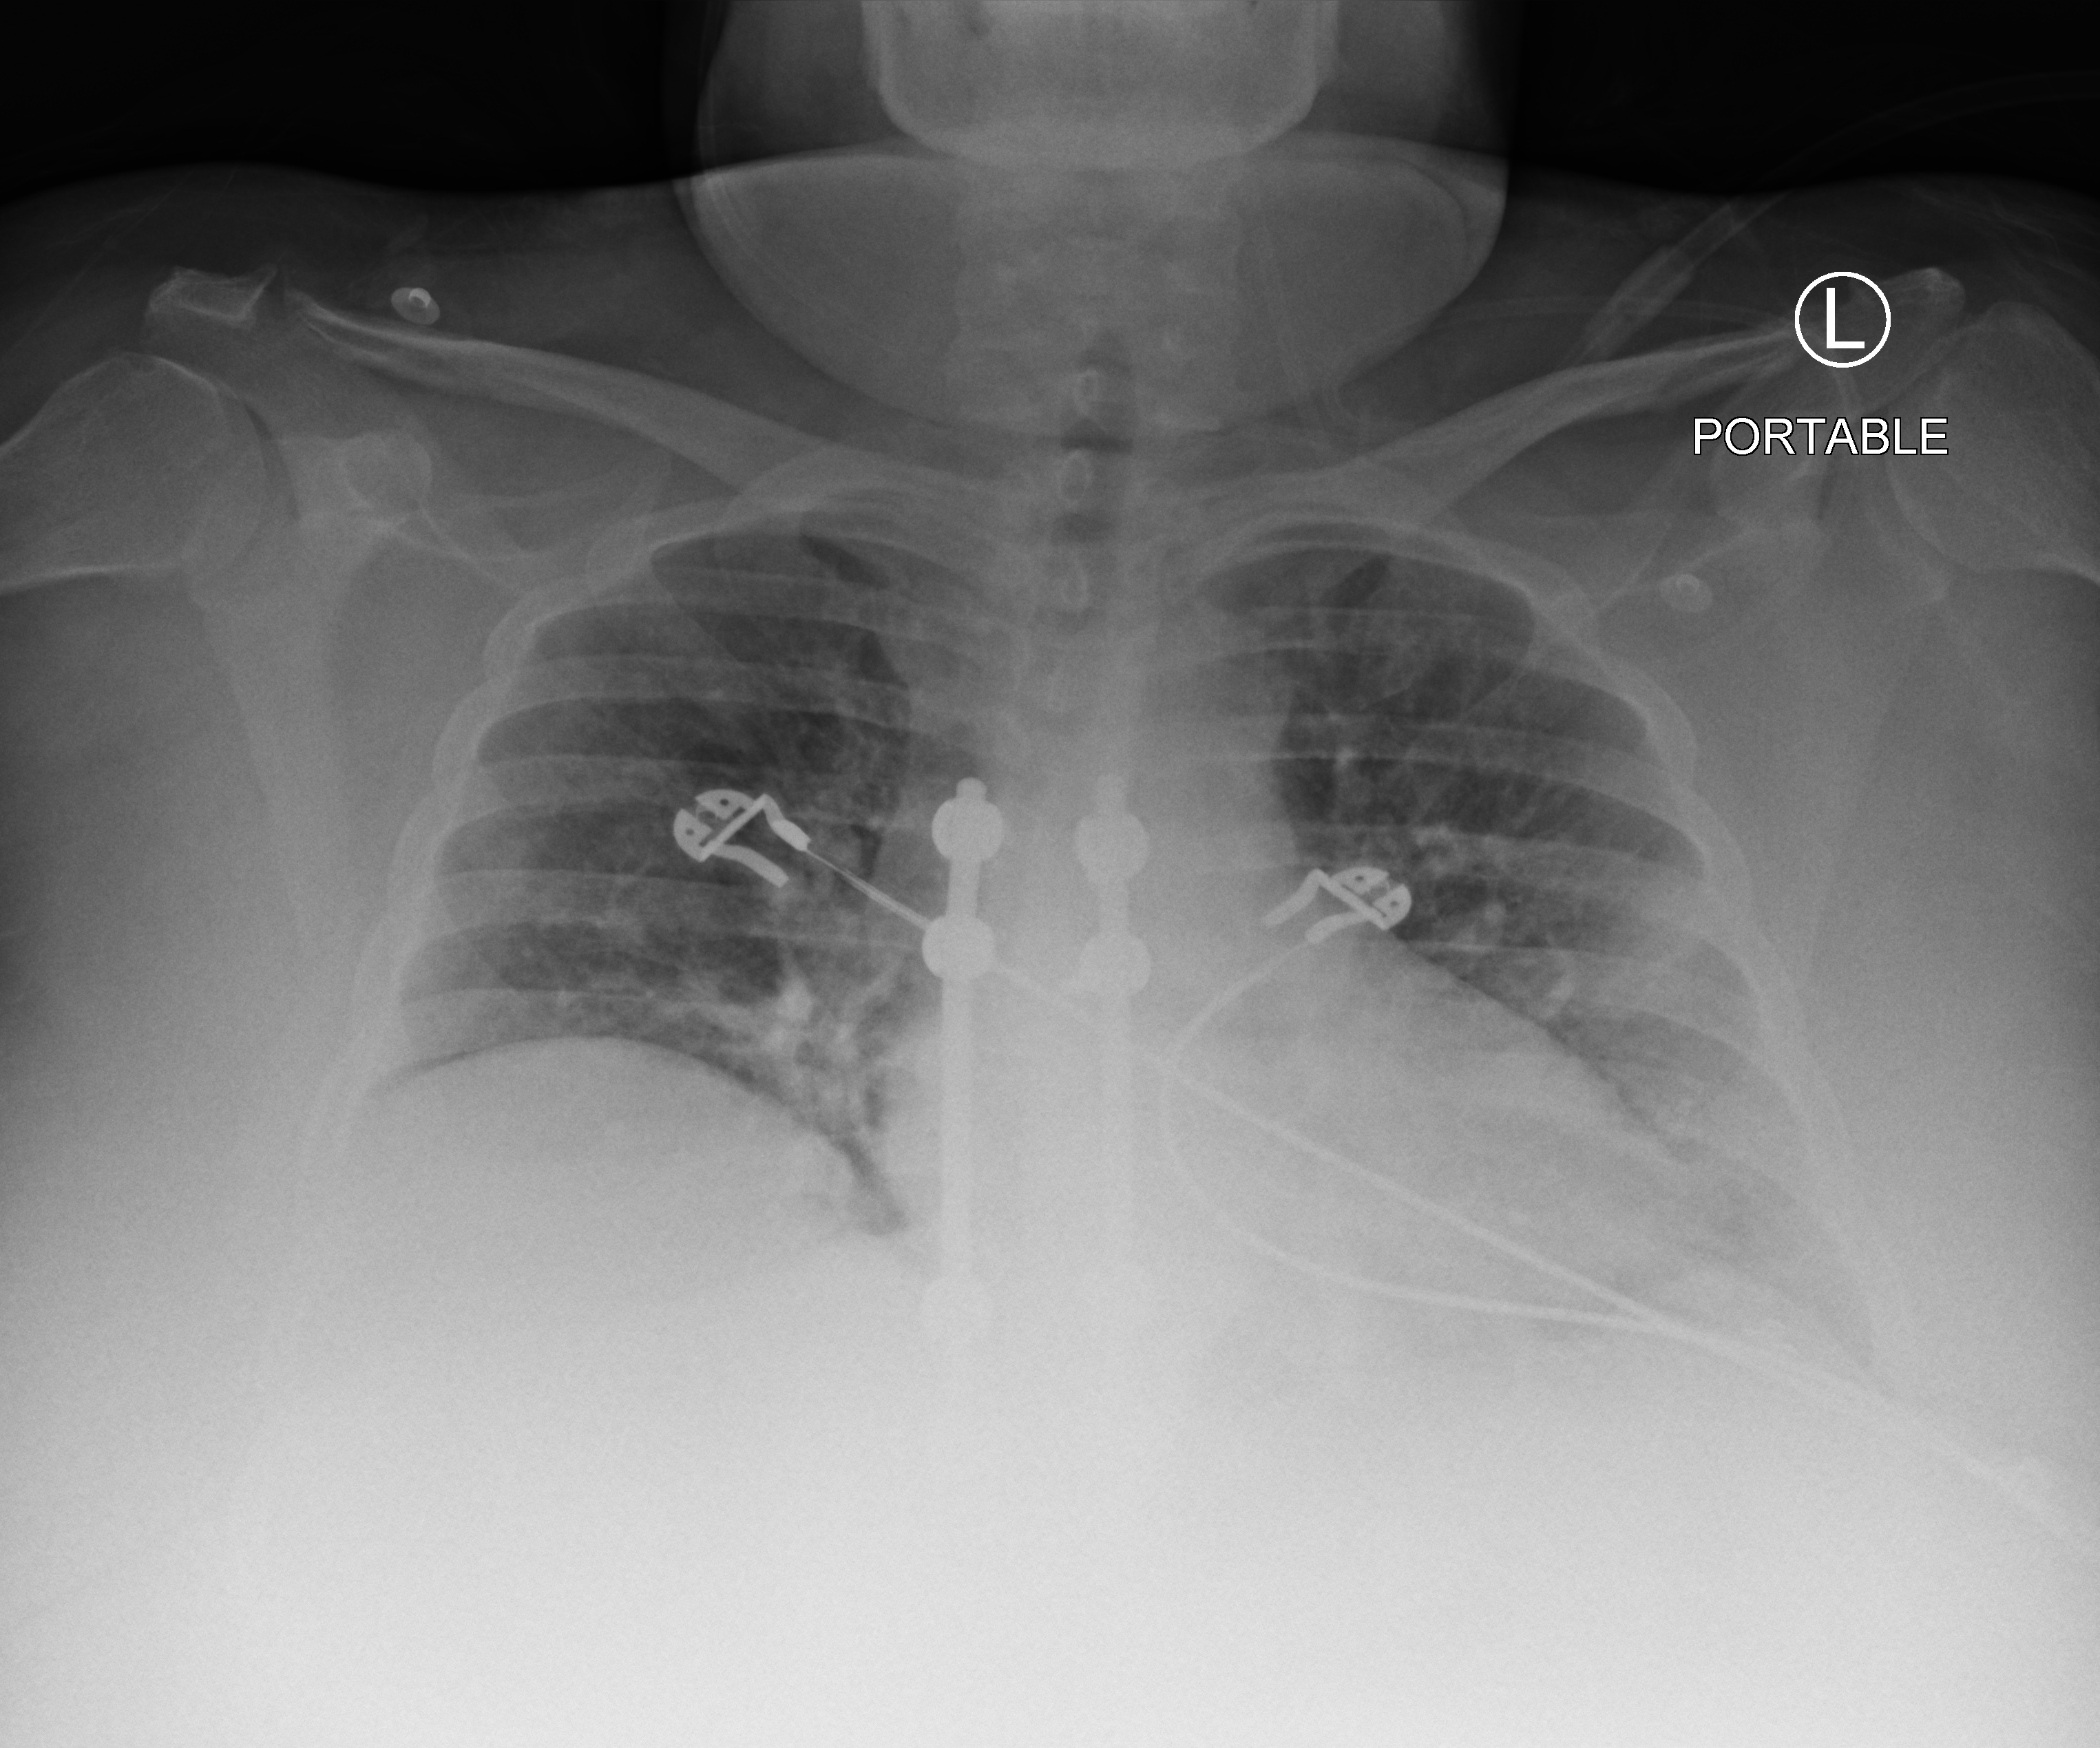
Chest X-ray (portable). Patient hospitalised with COVID-19; female, aged 18–59 years.
From the hospital-stay record, not from the radiograph (when in the stay this image was taken is not recorded): admitted to intensive care during this hospital stay: no; mechanically ventilated during this hospital stay: no.